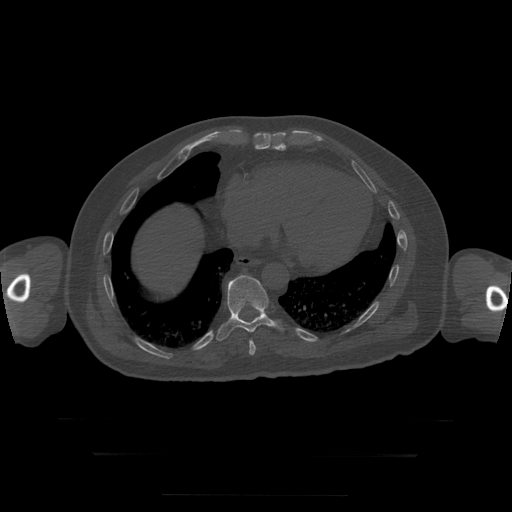
CT including the spine, one axial slice; 120 kVp; bone window (W 1800 / L 400 HU); 1.25 mm slice thickness; 512 × 512 image matrix. Patient age 73 years. From the clinical record (not read from this slice): primary cancer: prostate.
Outlined on this slice (semi-automatically segmented with operator editing):
- T10 vertebra: bounding box [x1, y1, x2, y2] px = [217, 276, 284, 341]
- T9 vertebra: [249, 340, 256, 356]